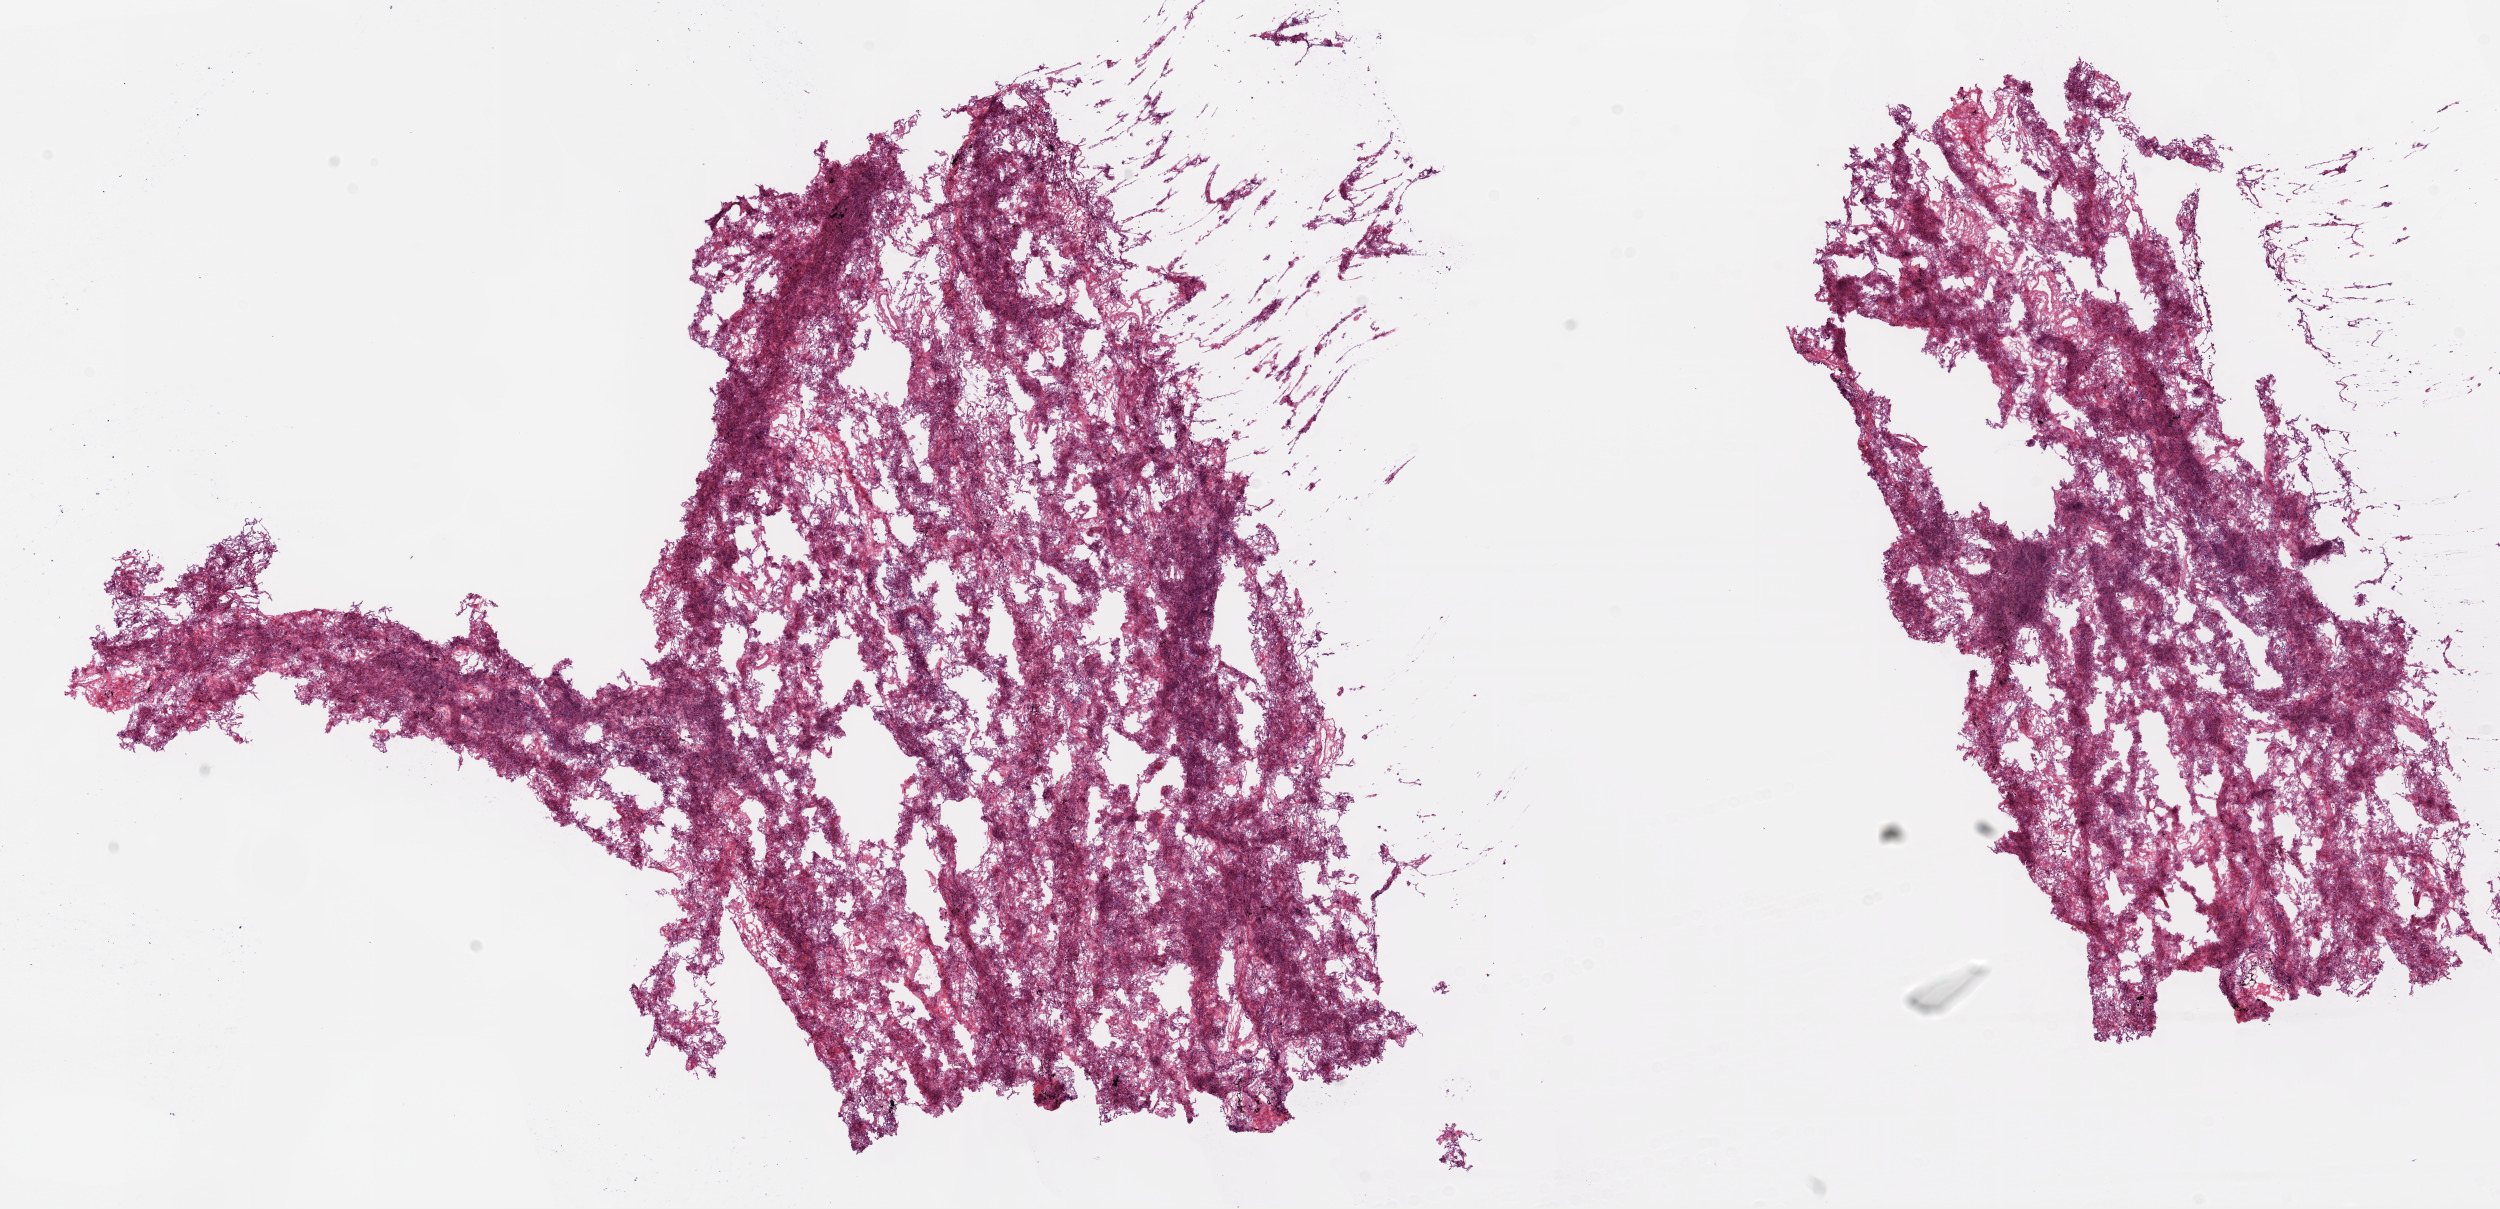
Digitized Hematoxylin and eosin (H&E) stained tissue section (whole slide), low-resolution overview of the scanned area, about 20.1 x 9.7 mm, frozen section from the bottom of the tissue portion, sample: solid tissue normal (non-tumour tissue), lung. Male, age 84 years at initial diagnosis.
* this section: solid tissue normal sample (biorepository sample class)
* patient diagnosis: Squamous cell carcinoma, NOS (upper lobe, lung)